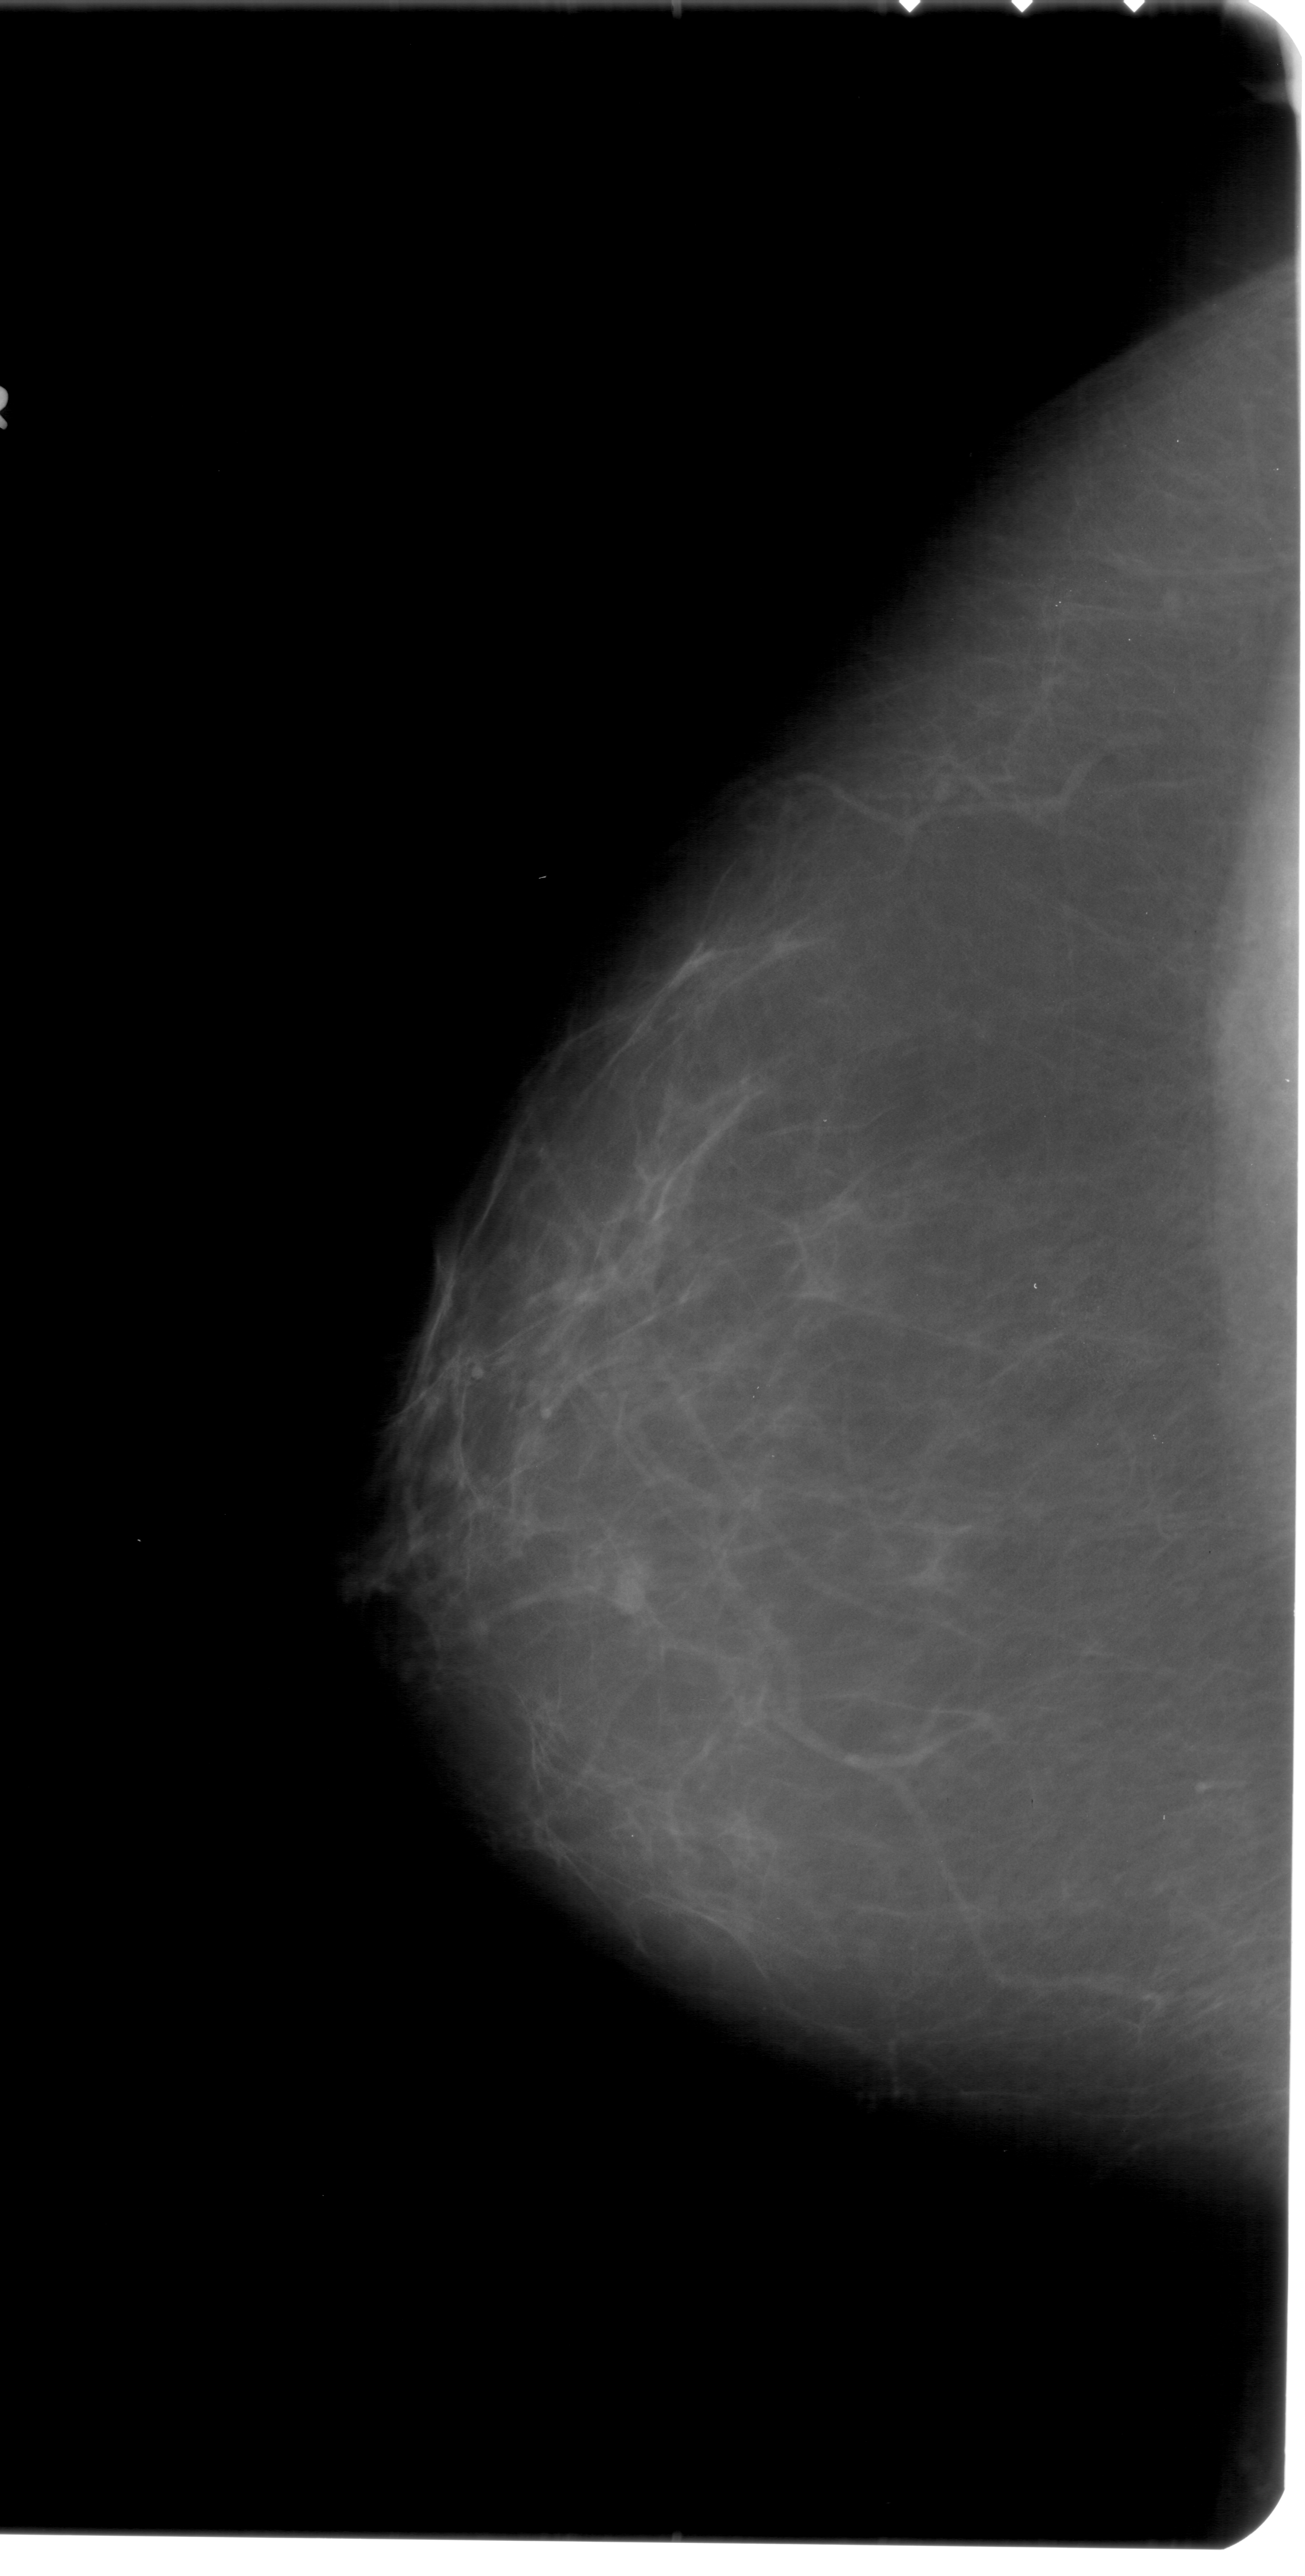
Digitized screen-film mammogram; left breast; craniocaudal (CC) view; BI-RADS breast density category 2 (scale 1–4).
Abnormality record for this image: mass, shape lobulated, margins ill defined; BI-RADS assessment category 4; subtlety rating 3 on a 1 (subtle) to 5 (obvious) scale; pathology (as recorded): benign.